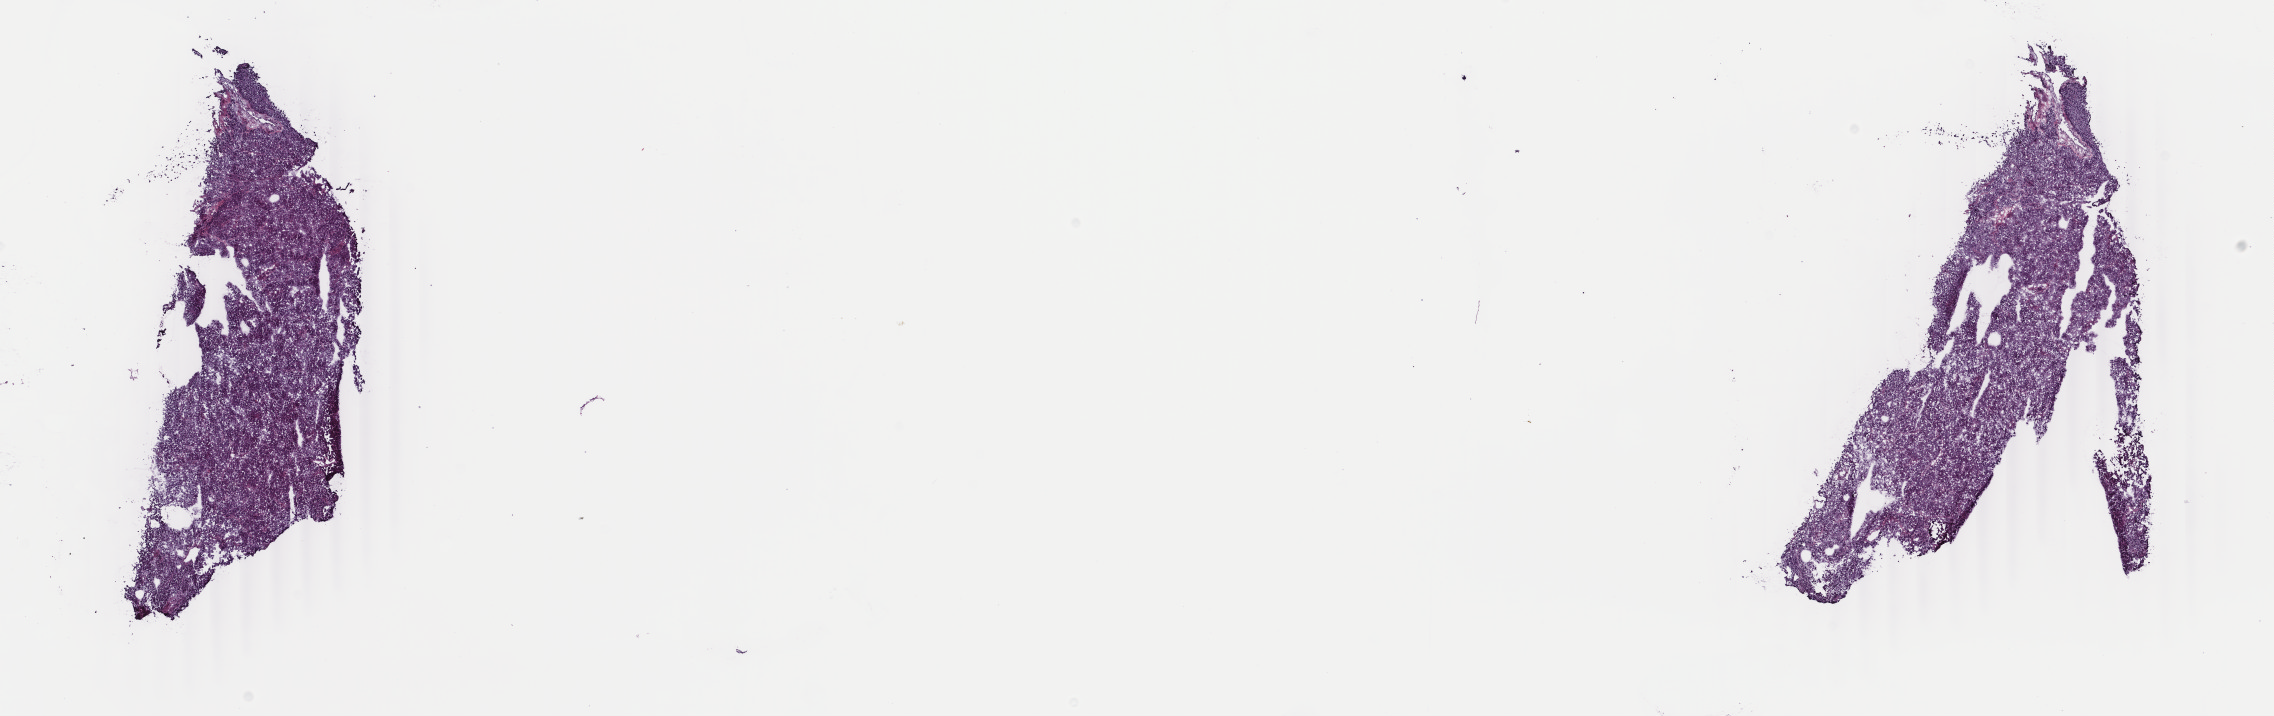
Whole-slide histology image, Hematoxylin and eosin (H&E) stained, a low-resolution overview of the entire scanned area, about 18.1 x 5.7 mm (slide scanned at 40x), frozen section from the top of the tissue portion, adrenal cortex, primary tumour sample. Patient: male, age at initial diagnosis 59 years. Pathologist review of this section (percent, as recorded): tumour cells 90%, tumour nuclei 90%, normal cells 0%, stromal cells 0%, necrosis 10%. Infiltration values recorded for this section: lymphocyte infiltration 40%, monocyte infiltration 20%, neutrophil infiltration 20%.
• pathologic diagnosis: Adrenal cortical carcinoma (cortex of adrenal gland)